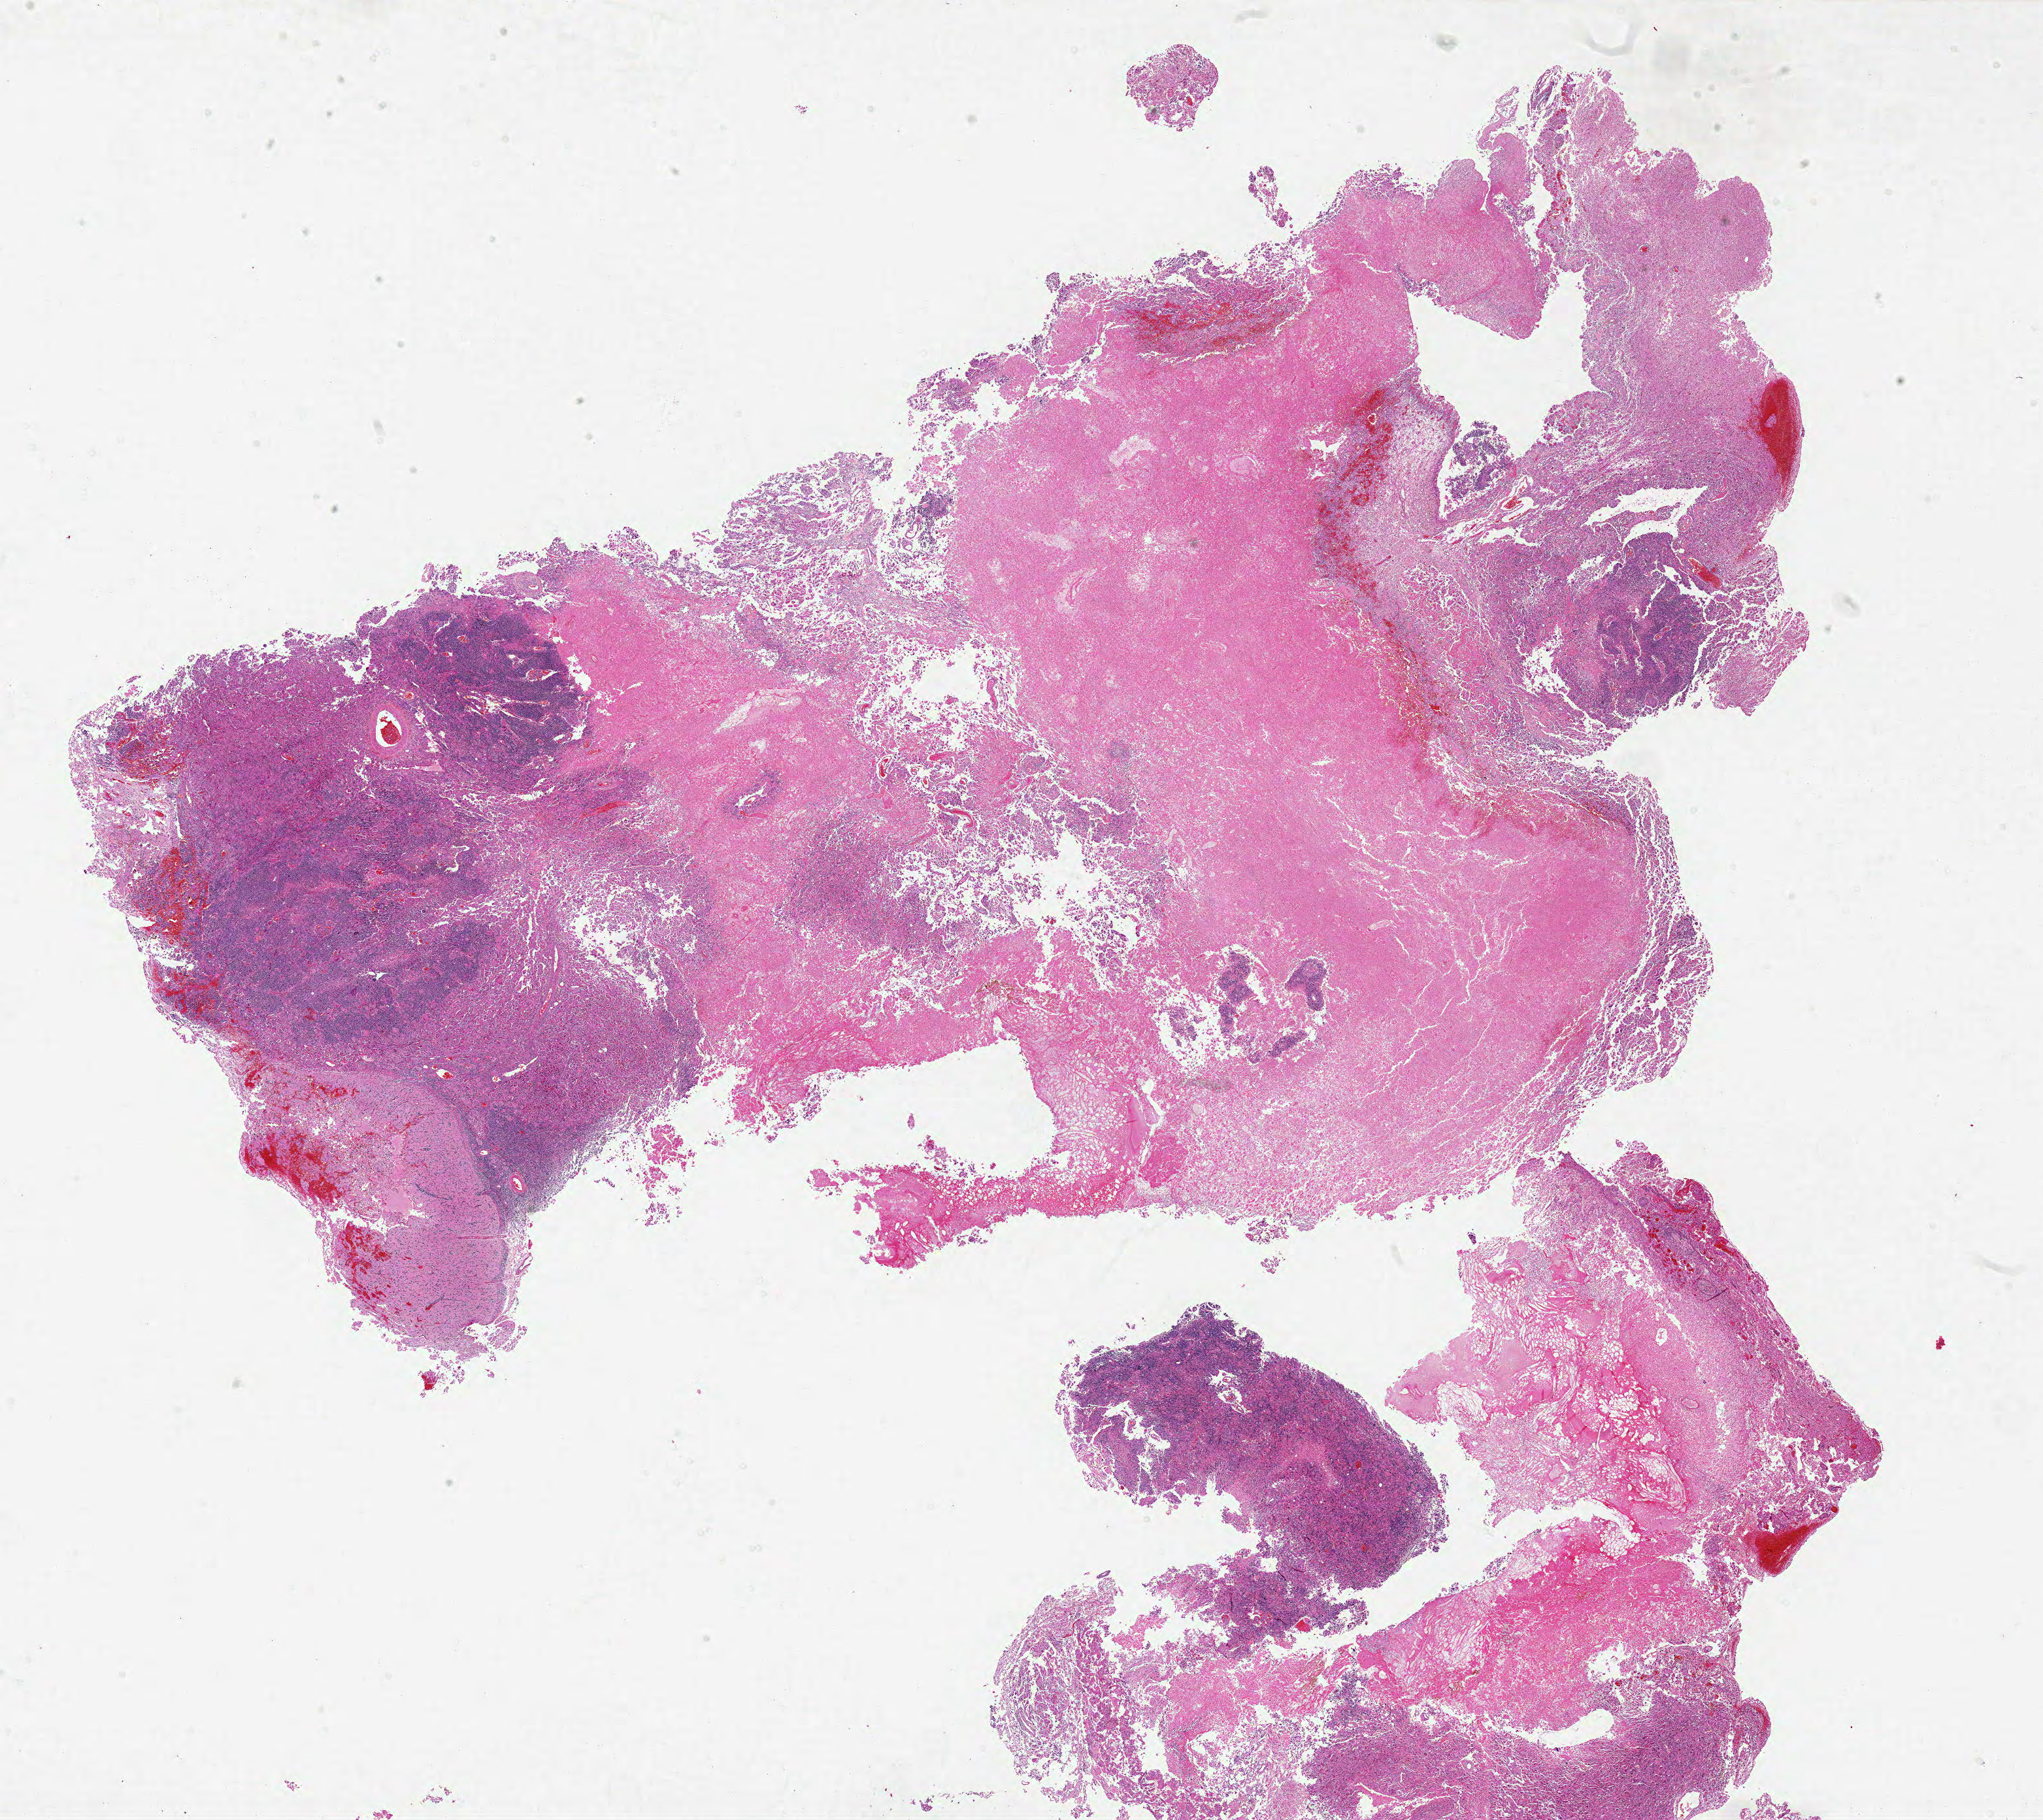
Digitized H&E-stained tissue section (whole slide) — whole scanned area (about 25.0 x 22.2 mm) shown as a low-resolution overview. FFPE section. Primary tumour sample from the brain. Male, age 24 years at initial diagnosis.
• histologic diagnosis: Glioblastoma